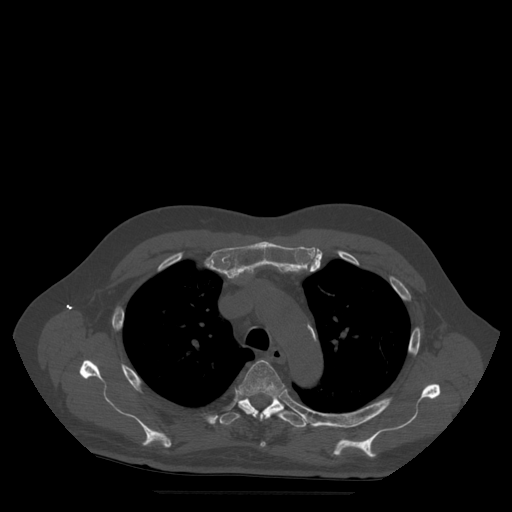
CT including the spine, one axial slice; slice 383 of 522 in the series (ordered by position); bone window (W 1800 / L 400 HU); 1.25 mm slice thickness; 512 × 512 image matrix. Patient age 72 years. Case-level facts recorded for this patient, not image findings: primary cancer: prostate.
Annotated regions visible in this slice (semi-automatic segmentation, software-assisted and operator-edited):
- T4 vertebra: bounding box [x1, y1, x2, y2] px = [237, 360, 286, 447]
- T5 vertebra: [220, 395, 308, 428]